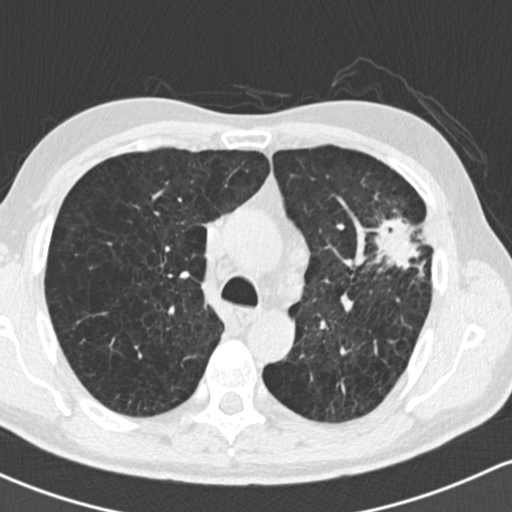
Low-dose screening chest CT, one axial slice. Slice 107 of 162 in the series (ordered by position). Reconstruction kernel B30f. 120 kVp. Lung window (W 1500 / L -600 HU). 2 mm slice thickness. 512 × 512 image matrix.
Structures marked on this image (manually delineated by an expert):
- lesion 1 (tumor, upper lobe of left lung): bounding box <374,217,432,270> (left, top, right, bottom; pixels)